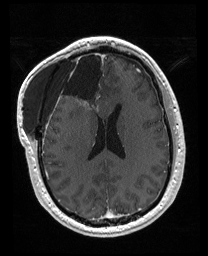
Brain MRI from a brain-tumour surgery series, one axial slice; position 75 of 176 along the scan axis; T1-weighted post-contrast; 1 mm slice thickness; 208 × 256 image matrix, field of view 208 × 256 mm. Case-level facts recorded for this patient, not image findings: histopathology: Astrocytoma; WHO grade: 4; IDH mutation: yes; tumour location: Right Orbitofrontal Anterior Temporal Insular.
Structures marked on this image (expert manual segmentation):
- previous resection cavity: bounding box <56,52,106,111> (left, top, right, bottom; pixels)